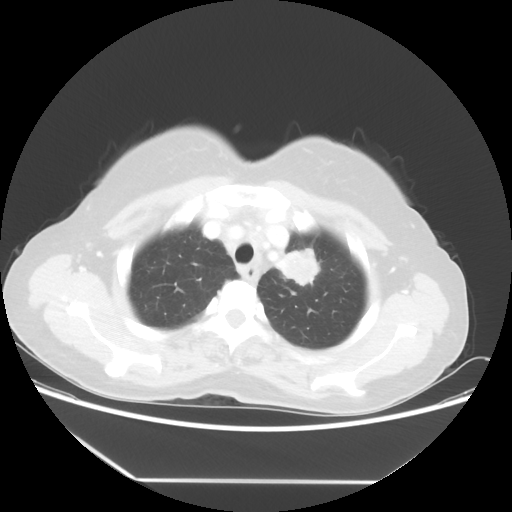
Chest CT, one axial slice; lung window (W 1500 / L -600 HU); 5 mm slice thickness; 512 × 512 image matrix. Patient: female, 50 years. From the clinical record (not read from this slice): clinical TNM (as recorded): T2 N3 M0.
Annotated regions visible in this slice (bounding box drawn by a radiologist):
- lung tumour (recorded histology: adenocarcinoma): bounding box <272,242,326,291> (left, top, right, bottom; pixels)